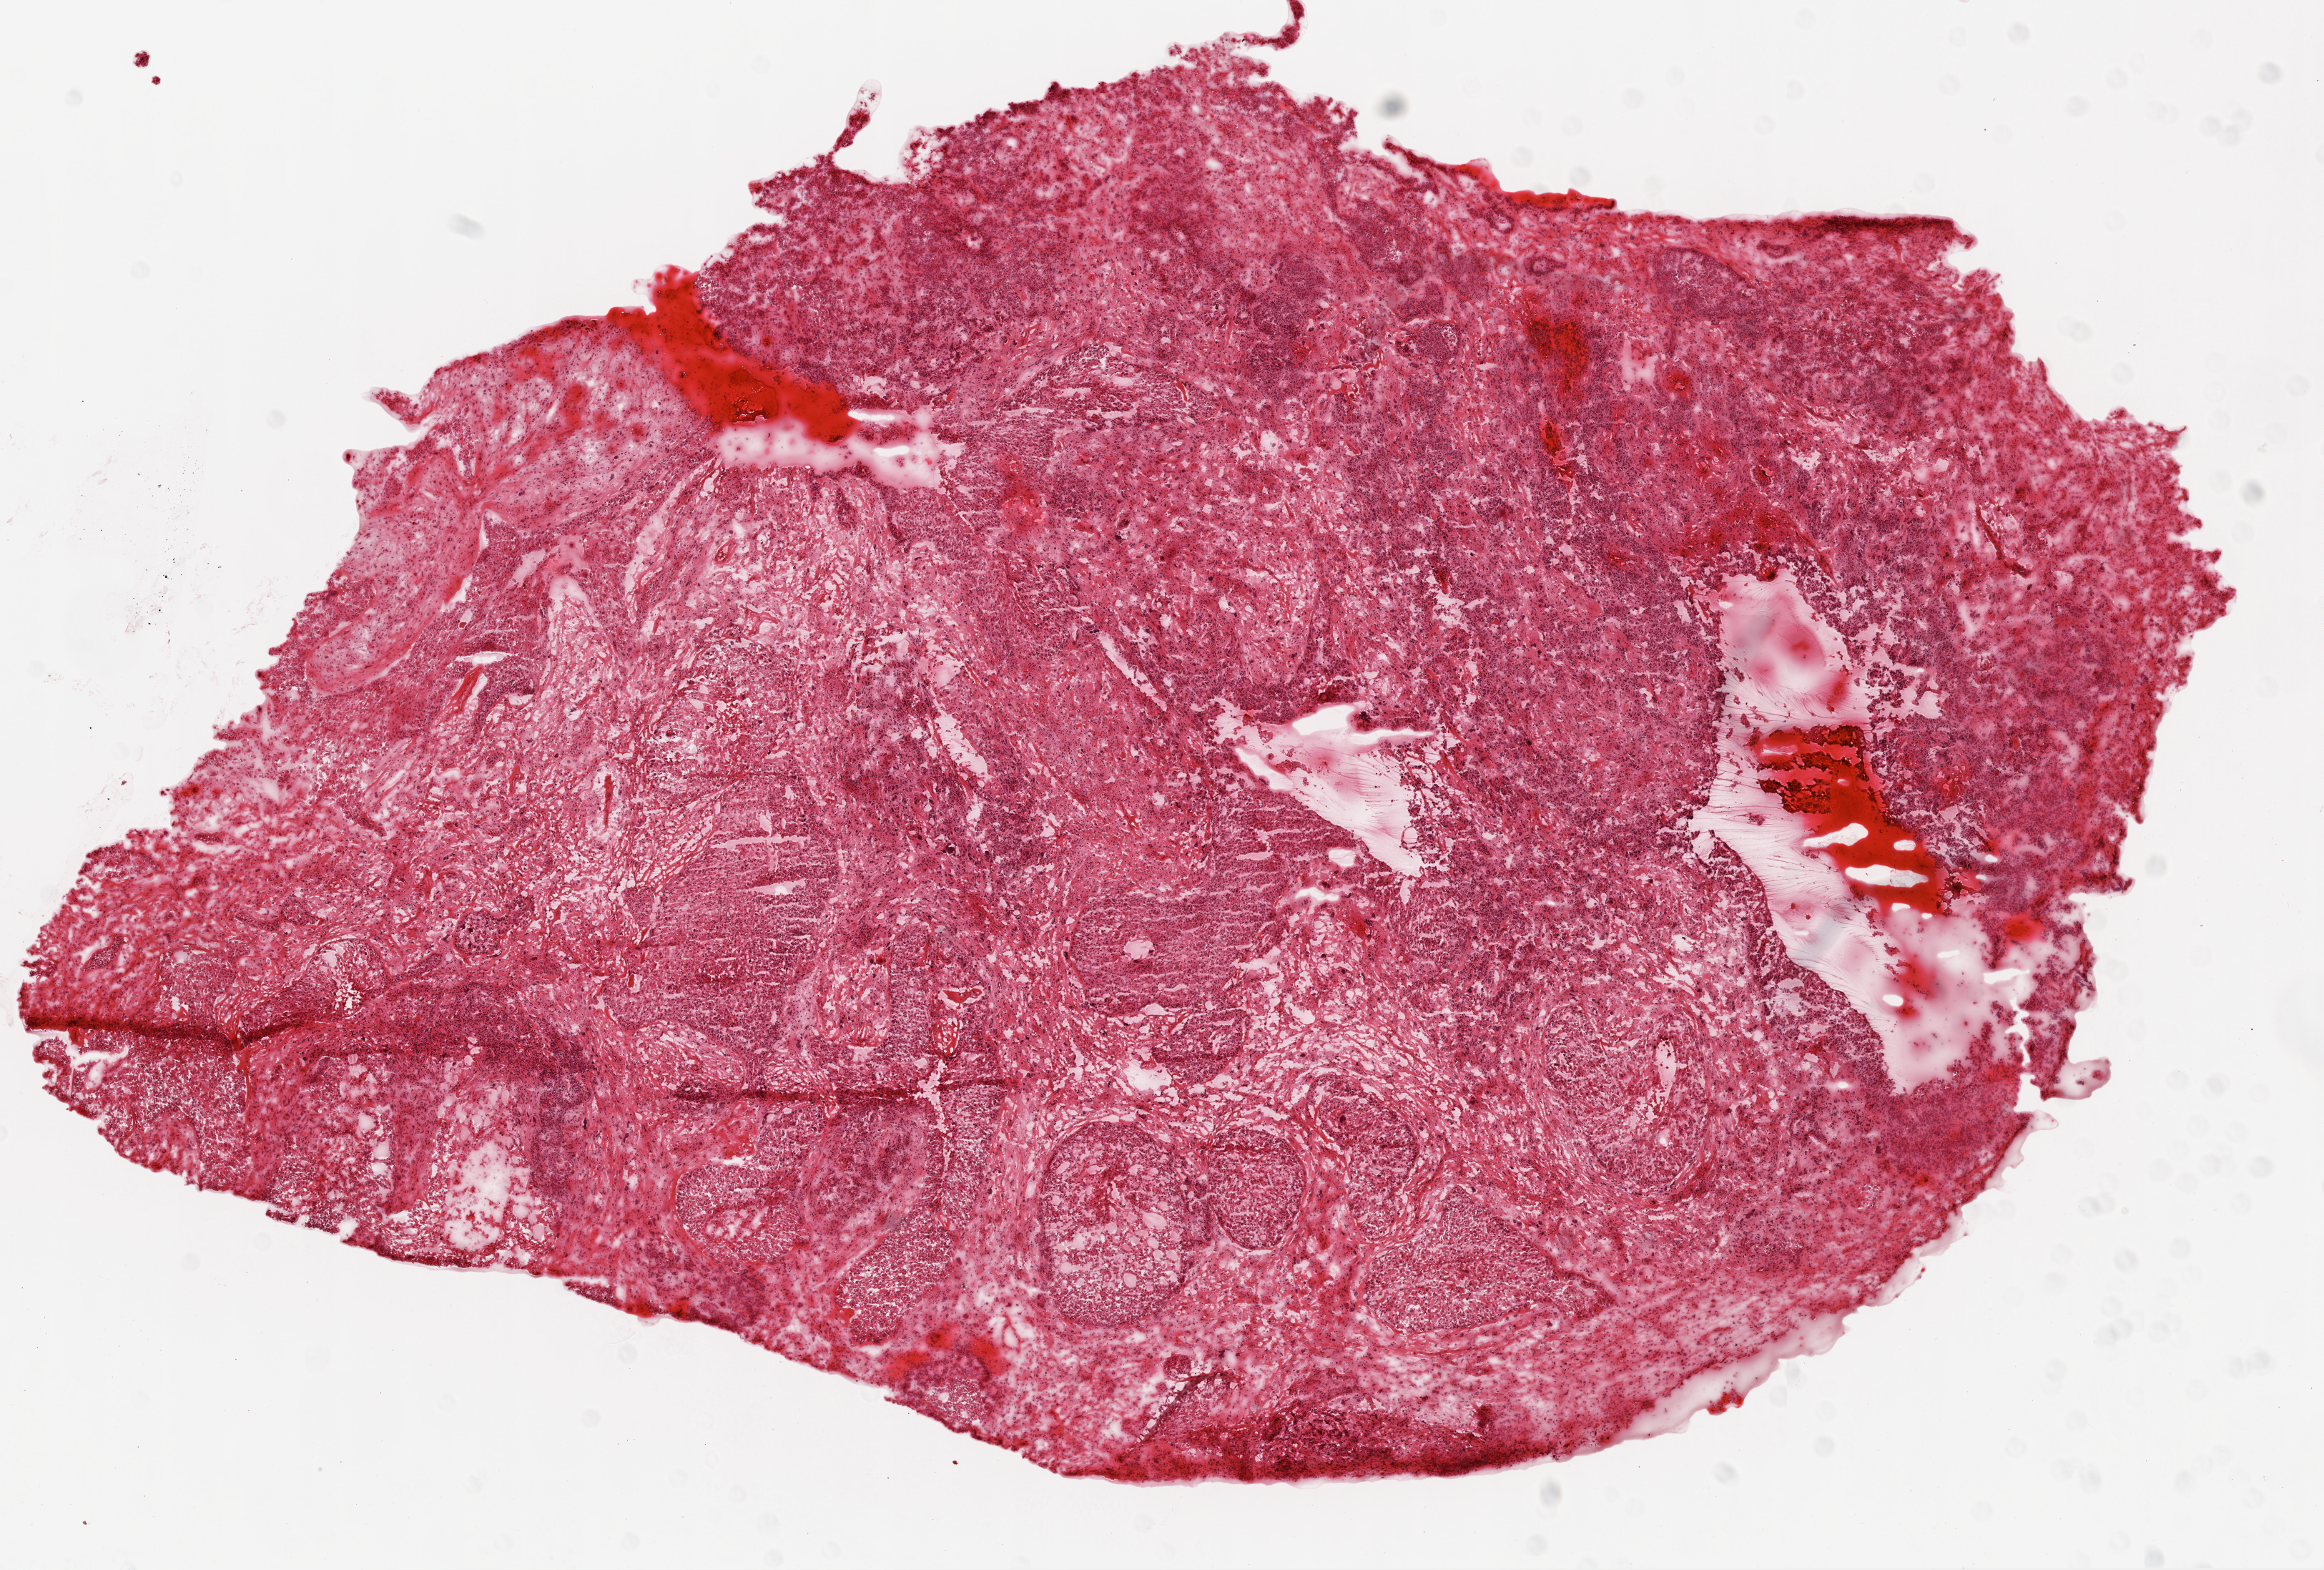
H&E-stained whole-slide image — shown as a low-resolution overview of the whole scanned area (about 13.0 x 8.8 mm); frozen section from the top of the tissue portion; ovary, primary tumour sample. Female, age 49 years at initial diagnosis. Histologic grade: G3 (poorly differentiated). Slide review estimates, as recorded: tumour cells 70%, tumour nuclei 80%, normal cells 0%, stromal cells 25%, necrosis 5%.
- FIGO stage: IIIC
- histologic diagnosis: Serous cystadenocarcinoma, NOS
- laterality: left